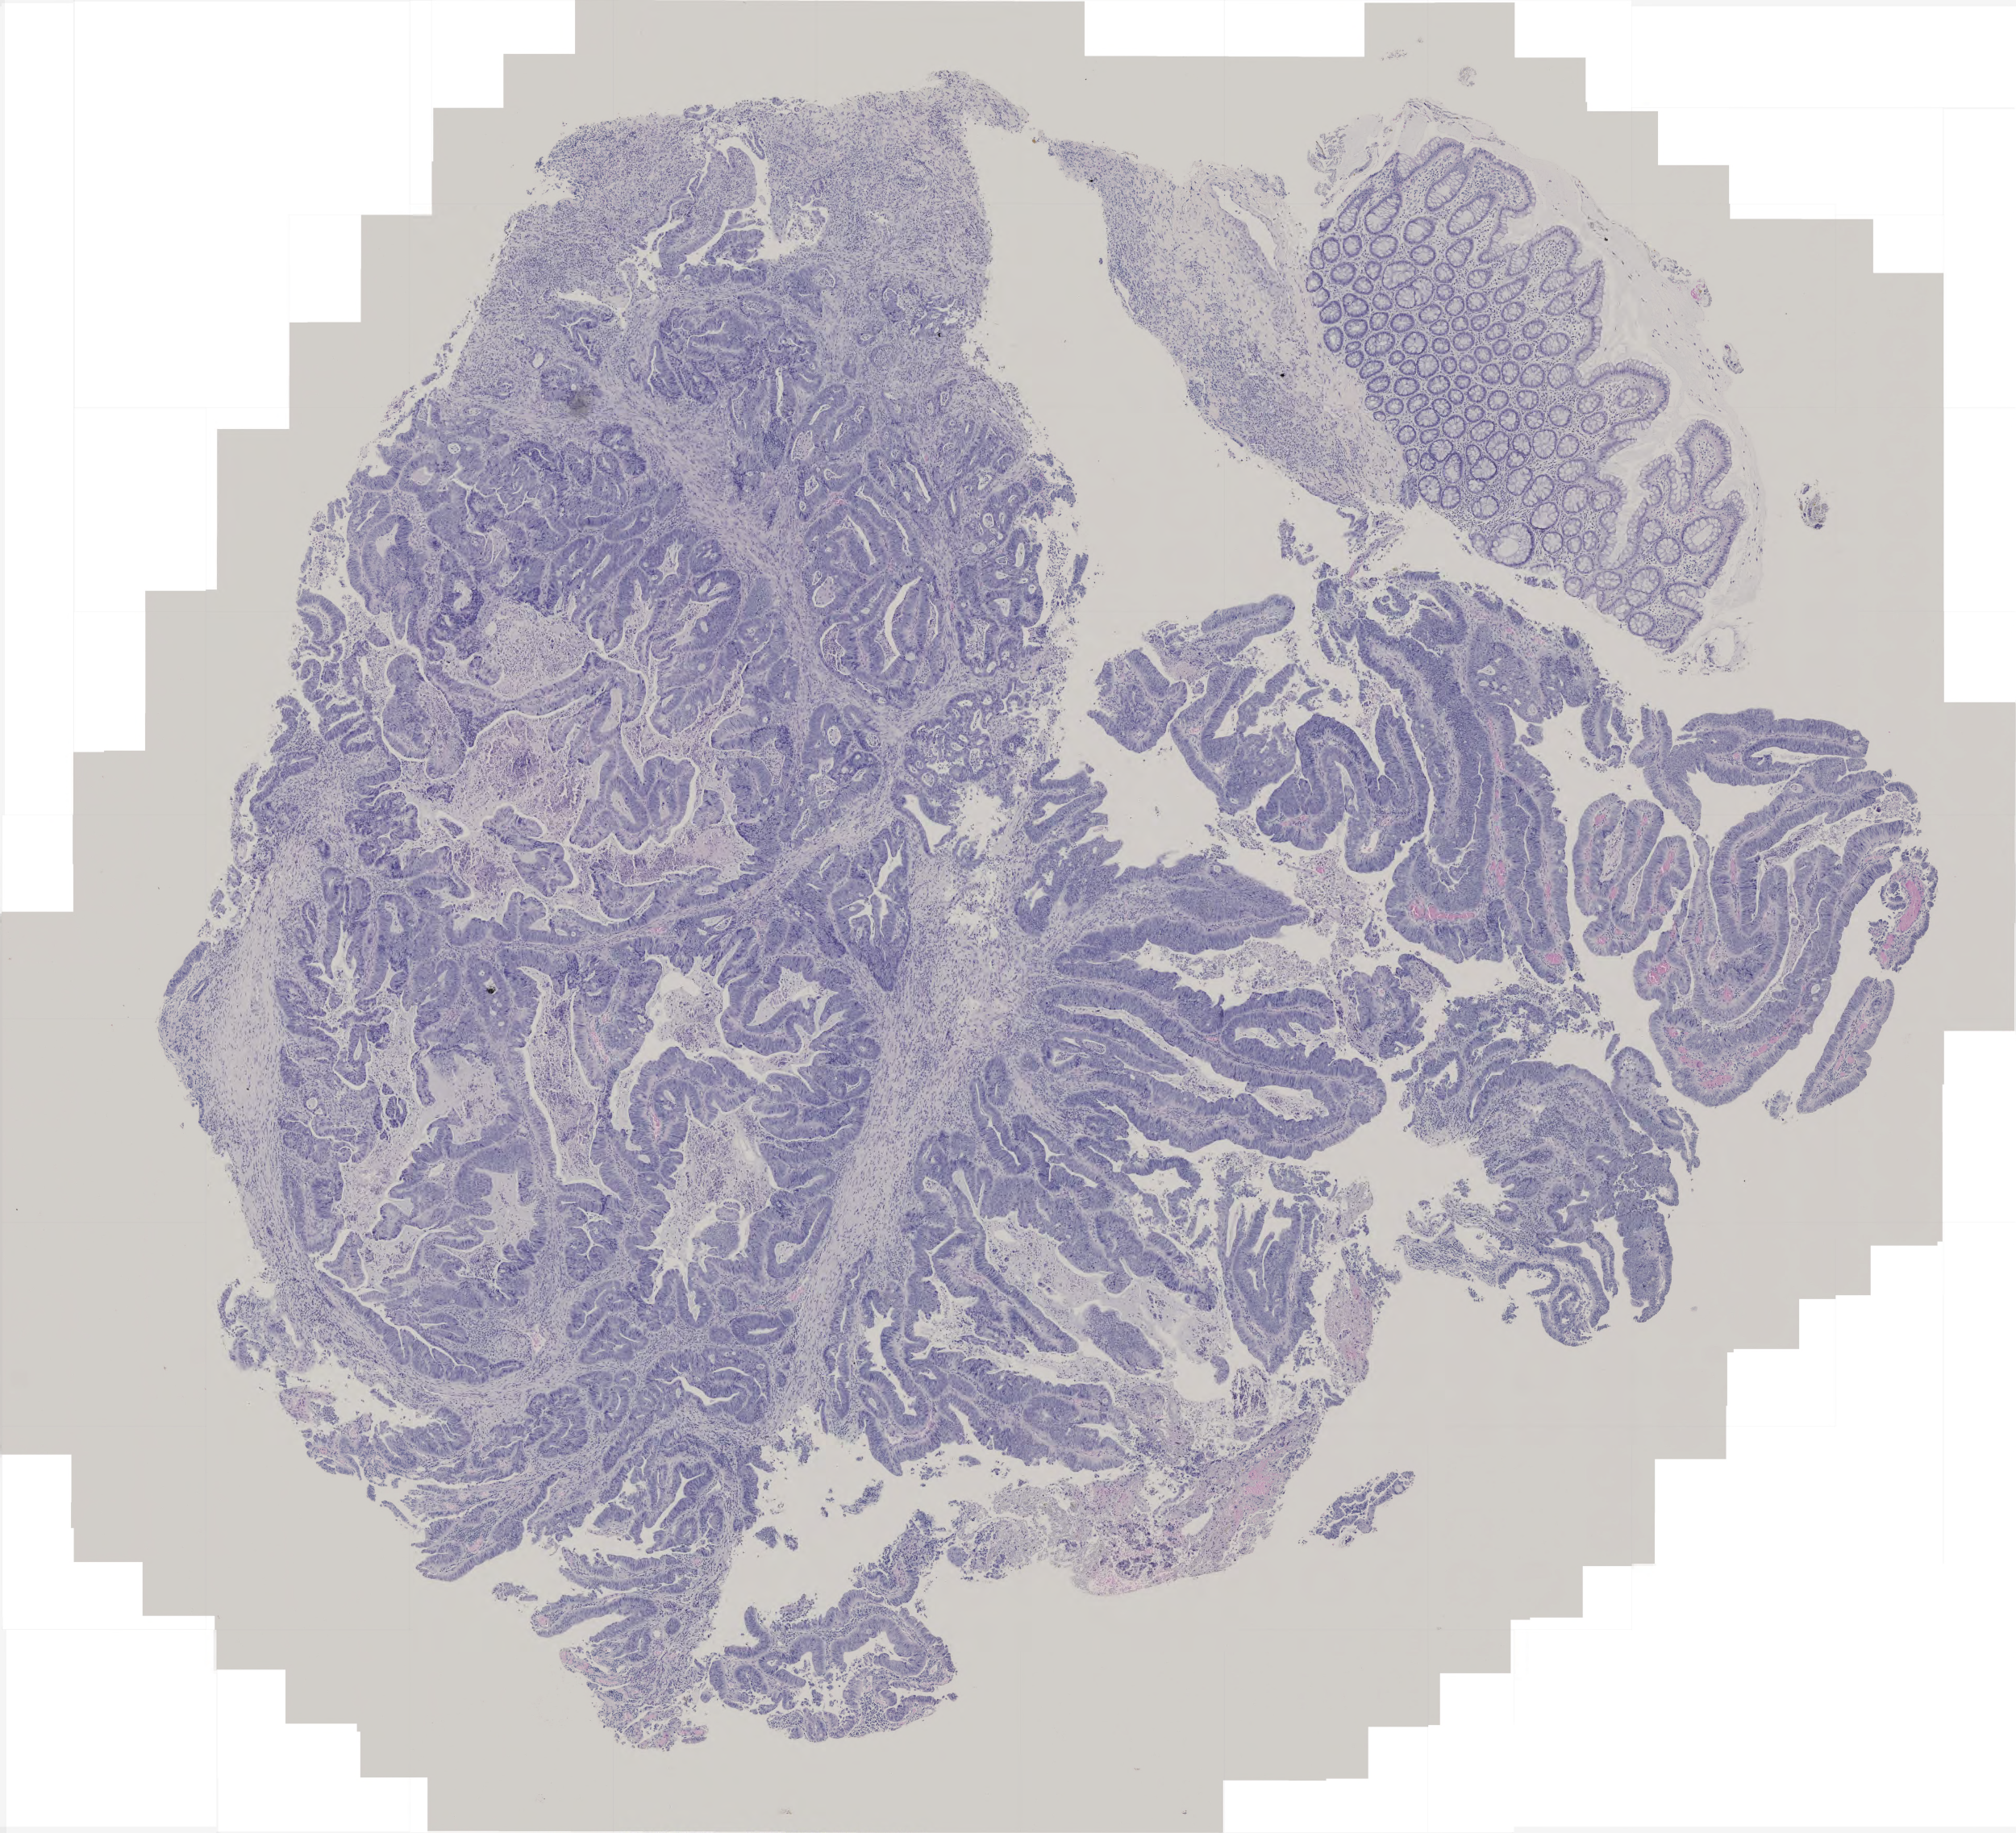
Whole-slide histology image, H&E — low-resolution overview of the scanned area, about 5.0 x 4.5 mm; formalin-fixed paraffin-embedded (FFPE) diagnostic section; sample: primary tumour, rectum. Female patient; age at initial diagnosis 66 years.
Lymph nodes positive (case pathology): 0 of 13 examined. Histologic diagnosis: Adenocarcinoma, NOS. AJCC pathologic stage: I (6th edition).